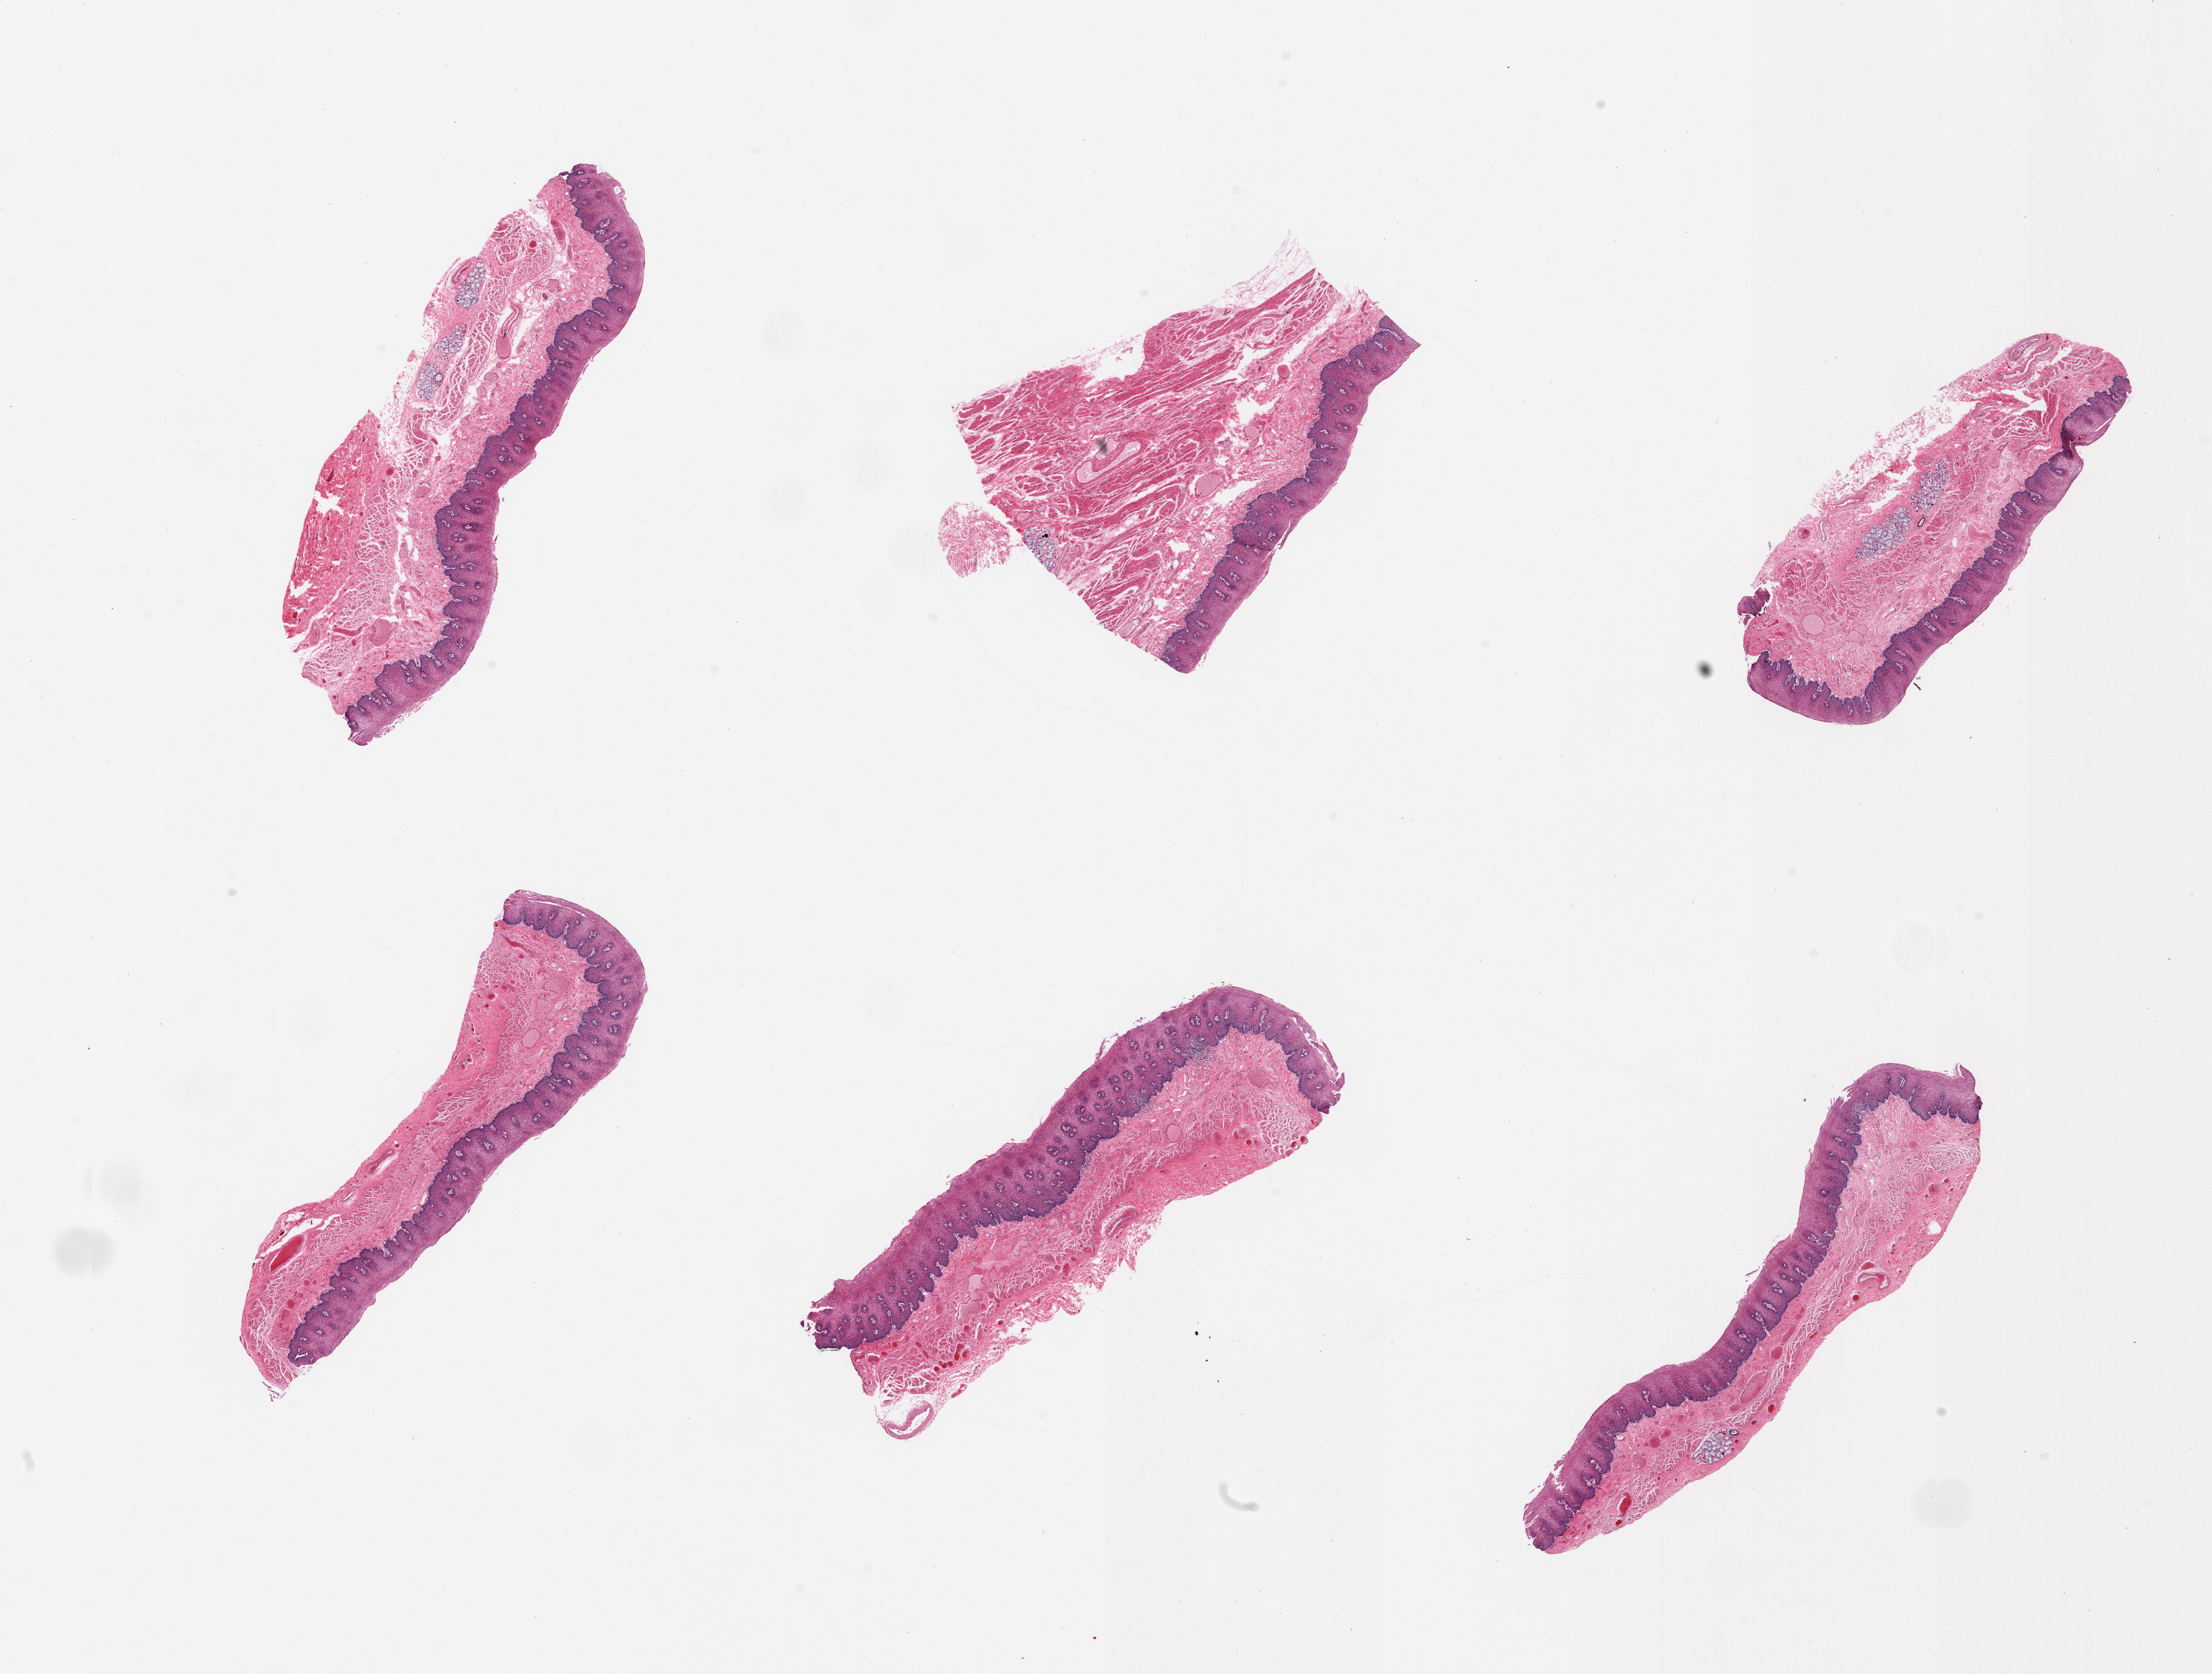
Whole-slide image, haematoxylin and eosin stain — a low-resolution overview of the entire scanned area, about 23.6 x 17.9 mm; PAXgene-fixed paraffin-embedded (PFPE) section; section of esophageal mucous membrane (target tissue); tissue donor sample. Male donor.
Review note (as recorded): 6 pieces; stratified squamous epithelium ~0.5mm thick; submucosal glands.